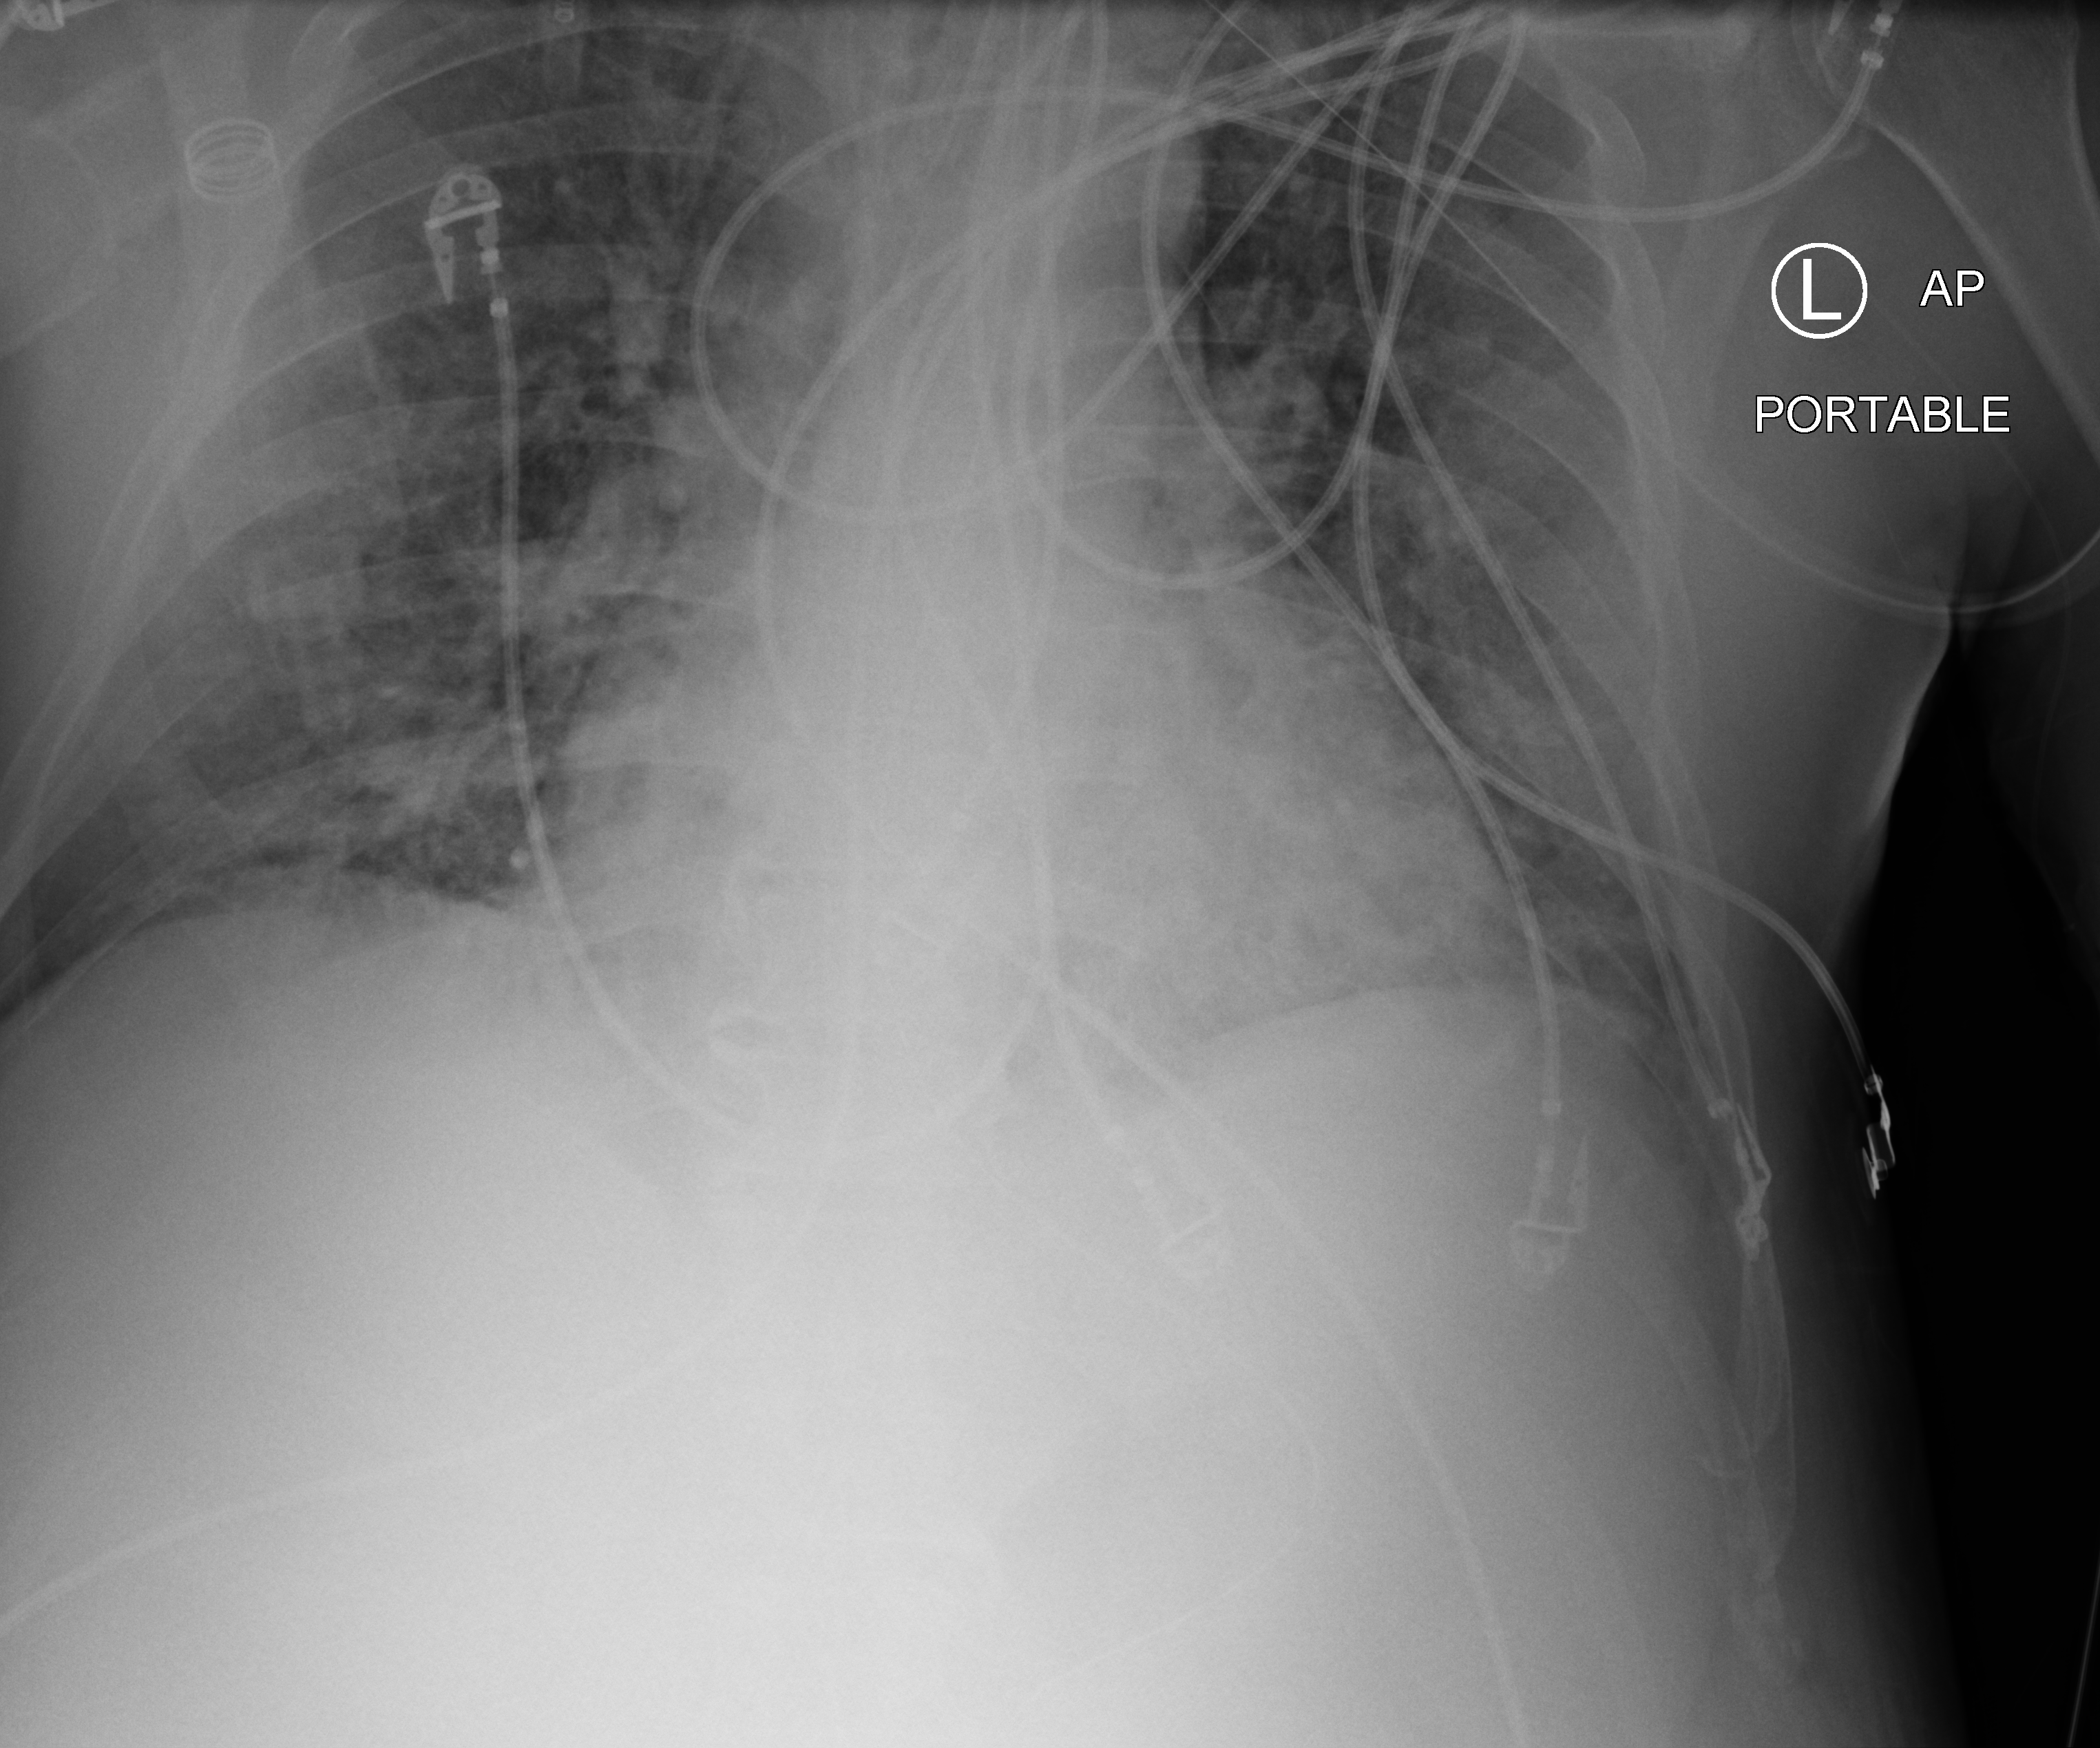
Portable chest radiograph; anteroposterior (AP) projection. Male patient hospitalised with COVID-19, age 18–59 years.
From the hospital-stay record, not from the radiograph (when in the stay this image was taken is not recorded): chronic kidney disease (admission record): no.